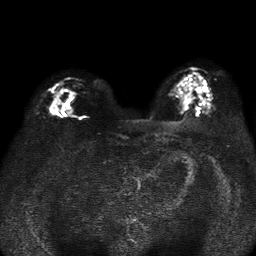
Breast MRI, one axial slice. Slice 22 of 37 in the series (ordered by position). Diffusion-weighted series; image 2 of 4 stored at this slice position (different b-values; order by instance number). 1.5 T. 5 mm slice thickness. 256 × 256 image matrix. Female patient.
Outlined on this slice (expert manual segmentation):
- tumour on diffusion-weighted imaging: bounding box (x1, y1, x2, y2) in pixels: (68, 88, 73, 95)